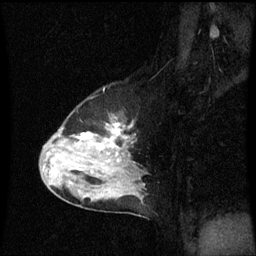
Breast MRI (dynamic contrast-enhanced), one sagittal slice. Position 42 of 60 along the scan axis. Dynamic contrast-enhanced series, image 2 of 3 at this slice position (ordered by acquisition). 1.5 T. TE 4.2 ms, TR 8.9 ms. 2 mm slice thickness. 256 × 256 image matrix, field of view 200 × 200 mm. Patient: female, 50 years. Case-level facts recorded for this patient, not image findings: setting: breast cancer imaged before/during neoadjuvant chemotherapy; receptor status: HR-positive, HER2-negative.
Annotated regions visible in this slice (semi-automatic segmentation, software-assisted and operator-edited):
- analysis volume of interest (the breast-tissue region the enhancement analysis was run in; not a lesion): box from (x=42, y=112) to (x=147, y=207) px
- tumour enhancement mask (voxels above the 70 % enhancement threshold inside the analysis volume of interest): (x=82, y=132)–(x=121, y=155)